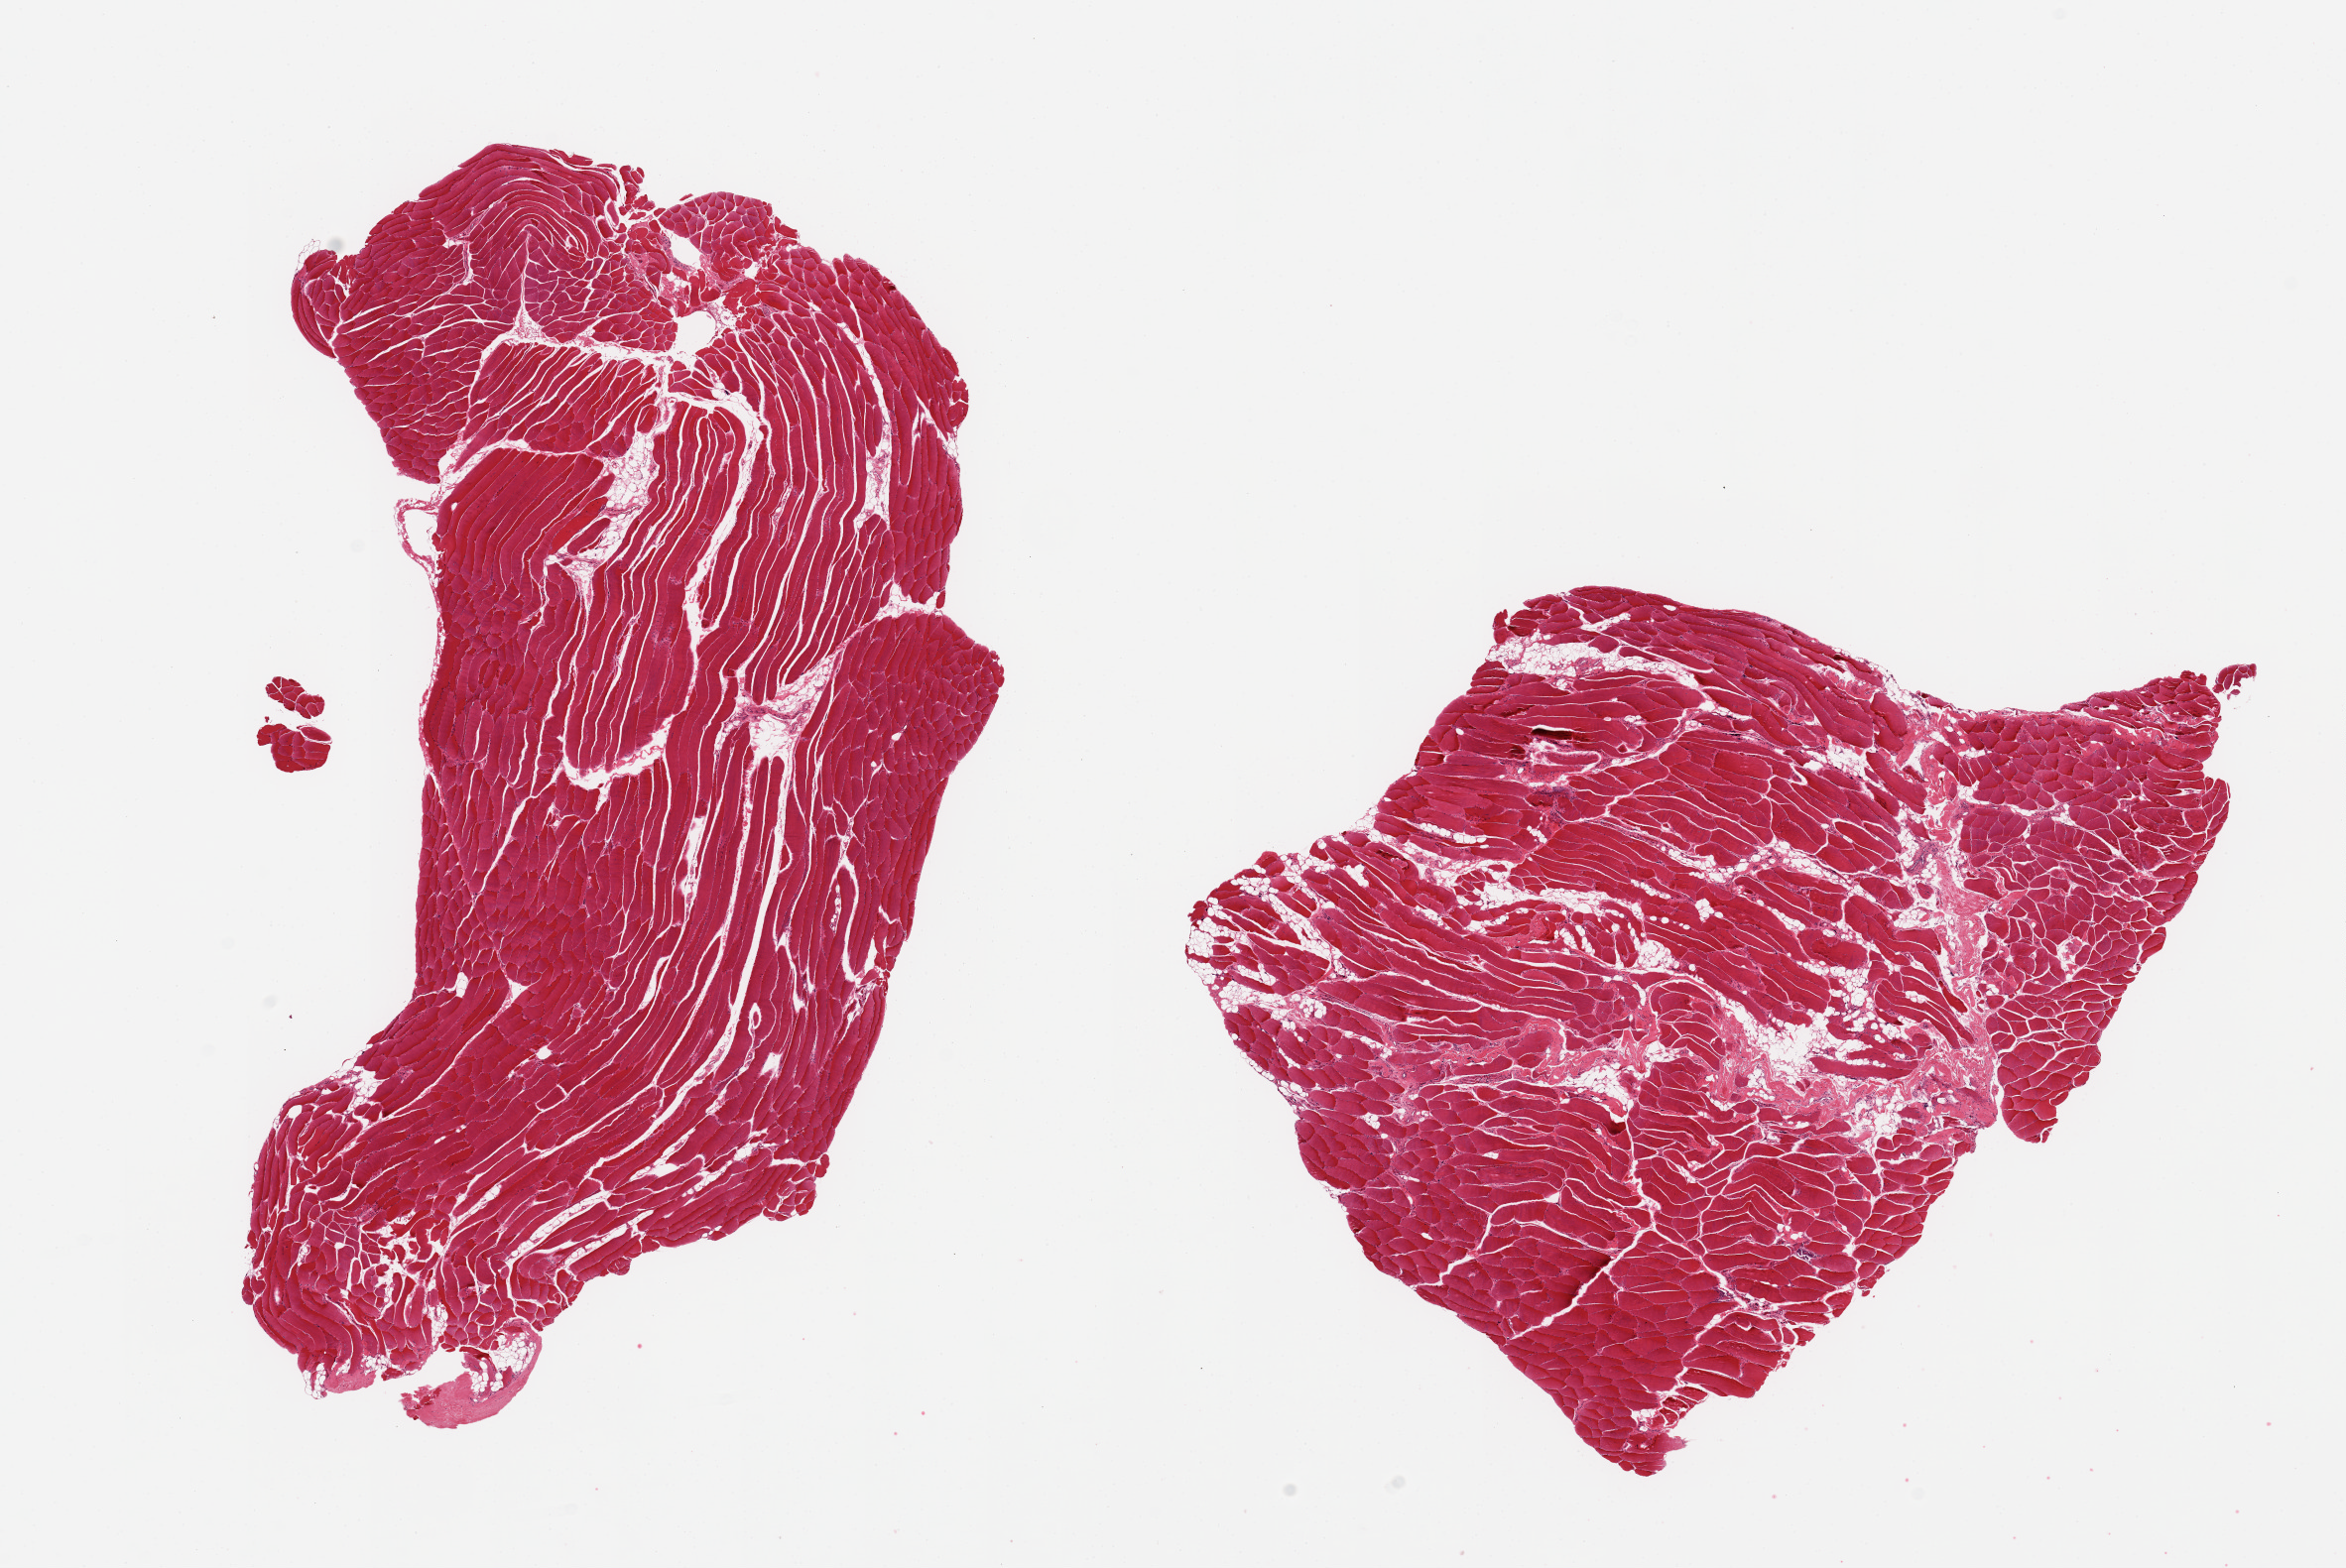
Whole-slide image, H&E stain, brightfield — shown as a low-resolution overview of the whole scanned area (about 18.7 x 12.5 mm, slide scanned at 20x). PAXgene-fixed, paraffin-embedded tissue. Section of skeletal muscle (target tissue). Tissue donor sample. Donor sex: male.
* review note (as recorded): 2 pieces, ~10% interstitial fat